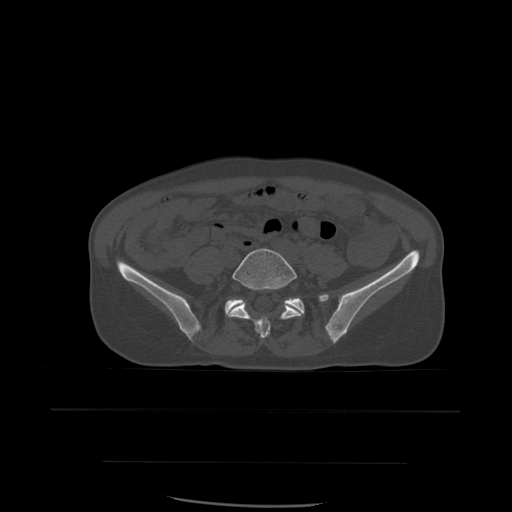
CT including the spine, one axial slice; position 142 of 574 along the scan axis; bone window (W 1800 / L 400 HU); 1.25 mm slice thickness; 512 × 512 image matrix, field of view 392 × 392 mm. Patient age 48 years. Case-level facts recorded for this patient, not image findings: primary cancer: lung.
Structures marked on this image (semi-automatic segmentation, software-assisted and operator-edited):
- L5 vertebra: bounding box (x1, y1, x2, y2) in pixels: (228, 248, 304, 339)